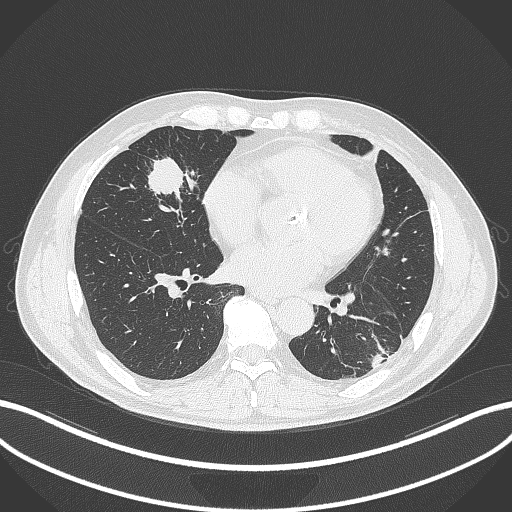
Chest CT, one axial slice; slice 117 of 399 in the series (ordered by position); reconstruction kernel B70f; 120 kVp; lung window (W 1500 / L -600 HU); 1 mm slice thickness; 512 × 512 image matrix, field of view 400 × 400 mm. Patient: male, 59 years. From the clinical record (not read from this slice): clinical TNM (as recorded): T2a N1 M0.
Structures marked on this image (rectangle marked by the reading radiologist):
- lung tumour (recorded histology: adenocarcinoma): bounding box (x1, y1, x2, y2) in pixels: (141, 154, 189, 207)